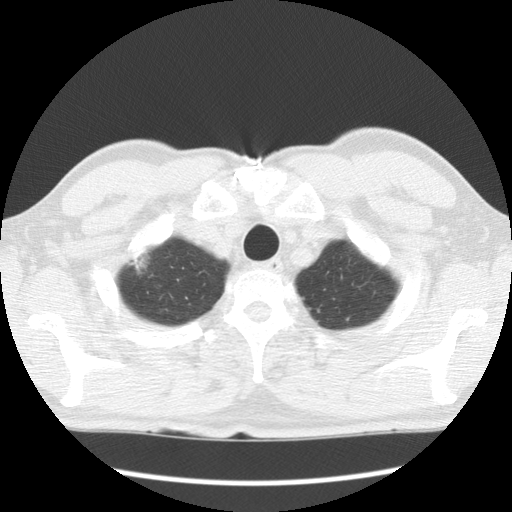
Axial slice from a low-dose chest CT screening exam. Baseline screening round. Lung window (W 1500 / L -600 HU). 2.5 mm slice thickness. 512 × 512 image matrix, field of view 340 × 340 mm. Male, age 64 years at enrolment.
Lesion marked by an expert reader, box from (x=111, y=225) to (x=168, y=286) px. The screening reader recorded 2 non-calcified nodules or masses ≥4 mm on this exam; which of them this box marks is not recorded. Participant outcome: lung cancer diagnosed 750 days after this screen — adenocarcinoma, NOS, right upper lobe, well differentiated (G1), stage IB (AJCC 6th edition), 45 mm at pathology.